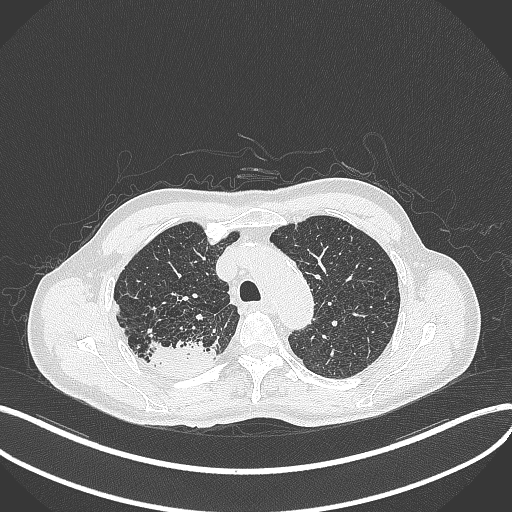
Chest CT, one axial slice. Slice 339 of 428 in the series (ordered by position). 120 kVp. Lung window (W 1500 / L -600 HU). 1 mm slice thickness. 512 × 512 image matrix, field of view 400 × 400 mm. Male patient, age 79 years. Case-level facts recorded for this patient, not image findings: clinical TNM (as recorded): T3 N0 M0.
Outlined on this slice (rectangle marked by the reading radiologist):
- lung tumour (recorded histology: adenocarcinoma): box from (x=144, y=336) to (x=221, y=376) px